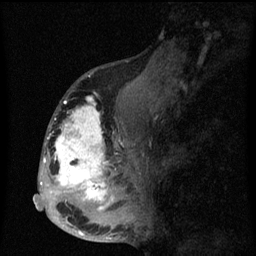
Breast MRI (dynamic contrast-enhanced), one sagittal slice; dynamic contrast-enhanced series, image 2 of 3 at this slice position (ordered by acquisition); 1.5 T; TE 4.2 ms, TR 8 ms; 256 × 256 image matrix. Patient: female, 50 years.
Structures marked on this image (semi-automatic segmentation, software-assisted and operator-edited):
- analysis volume of interest (the breast-tissue region the enhancement analysis was run in; not a lesion): bounding box <43,90,142,216> (left, top, right, bottom; pixels)
- tumour enhancement mask (voxels above the 70 % enhancement threshold inside the analysis volume of interest): <43,97,114,210>